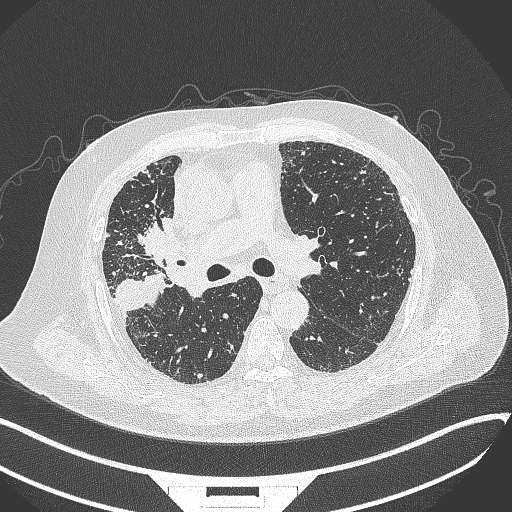
Chest CT, one axial slice; position 207 of 384 along the scan axis; 120 kVp; lung window (W 1500 / L -600 HU); 1 mm slice thickness; 512 × 512 image matrix, field of view 400 × 400 mm. Patient: male, 69 years. Case-level facts recorded for this patient, not image findings: clinical TNM (as recorded): T4 N3 M1.
Structures marked on this image (bounding box drawn by a radiologist):
- lung tumour (recorded histology: adenocarcinoma): box from (x=129, y=207) to (x=190, y=275) px